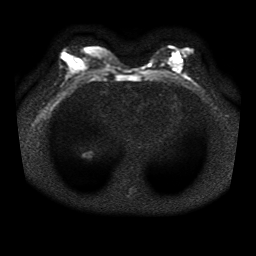
Breast MRI, one axial slice. Slice 17 of 41 in the series (ordered by position). Diffusion-weighted series; image 2 of 4 stored at this slice position (different b-values; order by instance number). 1.5 T. 5 mm slice thickness. 256 × 256 image matrix, field of view 330 × 330 mm. Female patient.
Structures marked on this image (outlined manually by an expert reader):
- tumour on diffusion-weighted imaging: bounding box (x1, y1, x2, y2) in pixels: (174, 54, 180, 62)